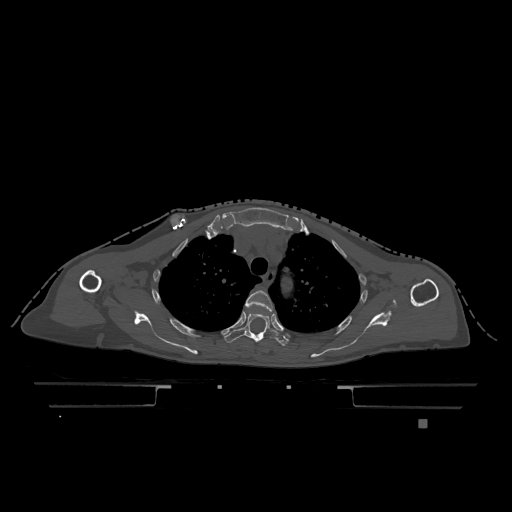
CT including the spine, one axial slice; slice 895 of 1317 in the series (ordered by position); bone window (W 1800 / L 400 HU); 0.5 mm slice thickness; 512 × 512 image matrix. Patient: female, 74 years. Case-level facts recorded for this patient, not image findings: primary cancer: lung.
Annotated regions visible in this slice (semi-automatic segmentation, software-assisted and operator-edited):
- T3 vertebra: bounding box (x1, y1, x2, y2) in pixels: (246, 290, 273, 311)
- T4 vertebra: (224, 312, 289, 346)